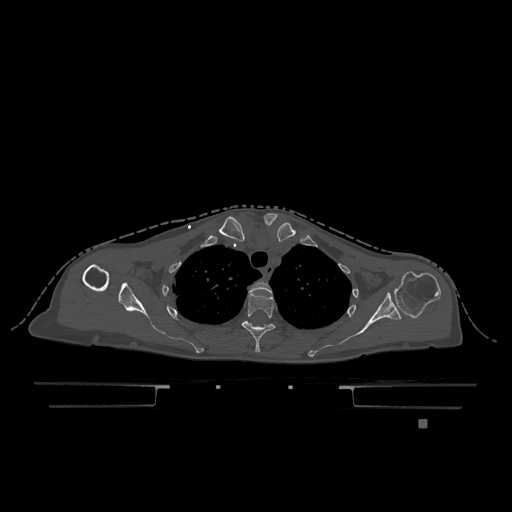
CT including the spine, one axial slice. Slice 923 of 1317 in the series (ordered by position). Bone window (W 1800 / L 400 HU). 512 × 512 image matrix. Patient: female, 74 years. Case-level facts recorded for this patient, not image findings: primary cancer: lung; vertebrae with lytic lesions (as recorded): T1, T4, T5, T6, L4, L5.
Annotated regions visible in this slice (semi-automatic segmentation, software-assisted and operator-edited):
- T2 vertebra: bounding box [x1, y1, x2, y2] px = [249, 282, 272, 293]
- T3 vertebra: [241, 293, 275, 353]
- T4 vertebra: [247, 321, 251, 324]